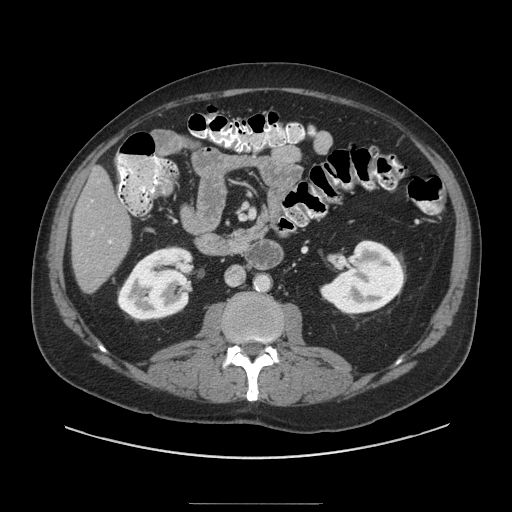
Contrast-enhanced abdominal CT (liver protocol), one axial slice; slice 29 of 91 in the series (ordered by position); reconstruction kernel STANDARD; 140 kVp; soft-tissue window (W 400 / L 40 HU); 512 × 512 image matrix. Case-level facts recorded for this patient, not image findings: diagnosis: hepatocellular carcinoma (patient treated with transarterial chemoembolisation; whether this scan precedes or follows treatment is not stated here); TNM stage (as recorded): Stage-I; Child-Pugh class: A; tumour differentiation: well differentiated; tumour nodularity: uninodular.
Outlined on this slice (semi-automatic segmentation, software-assisted and operator-edited):
- liver parenchyma outside the tumour (the mass and vessels are separate outlines, so this box may not span the whole liver): bounding box (x1, y1, x2, y2) in pixels: (72, 166, 130, 292)
- liver vessels: (91, 233, 112, 243)